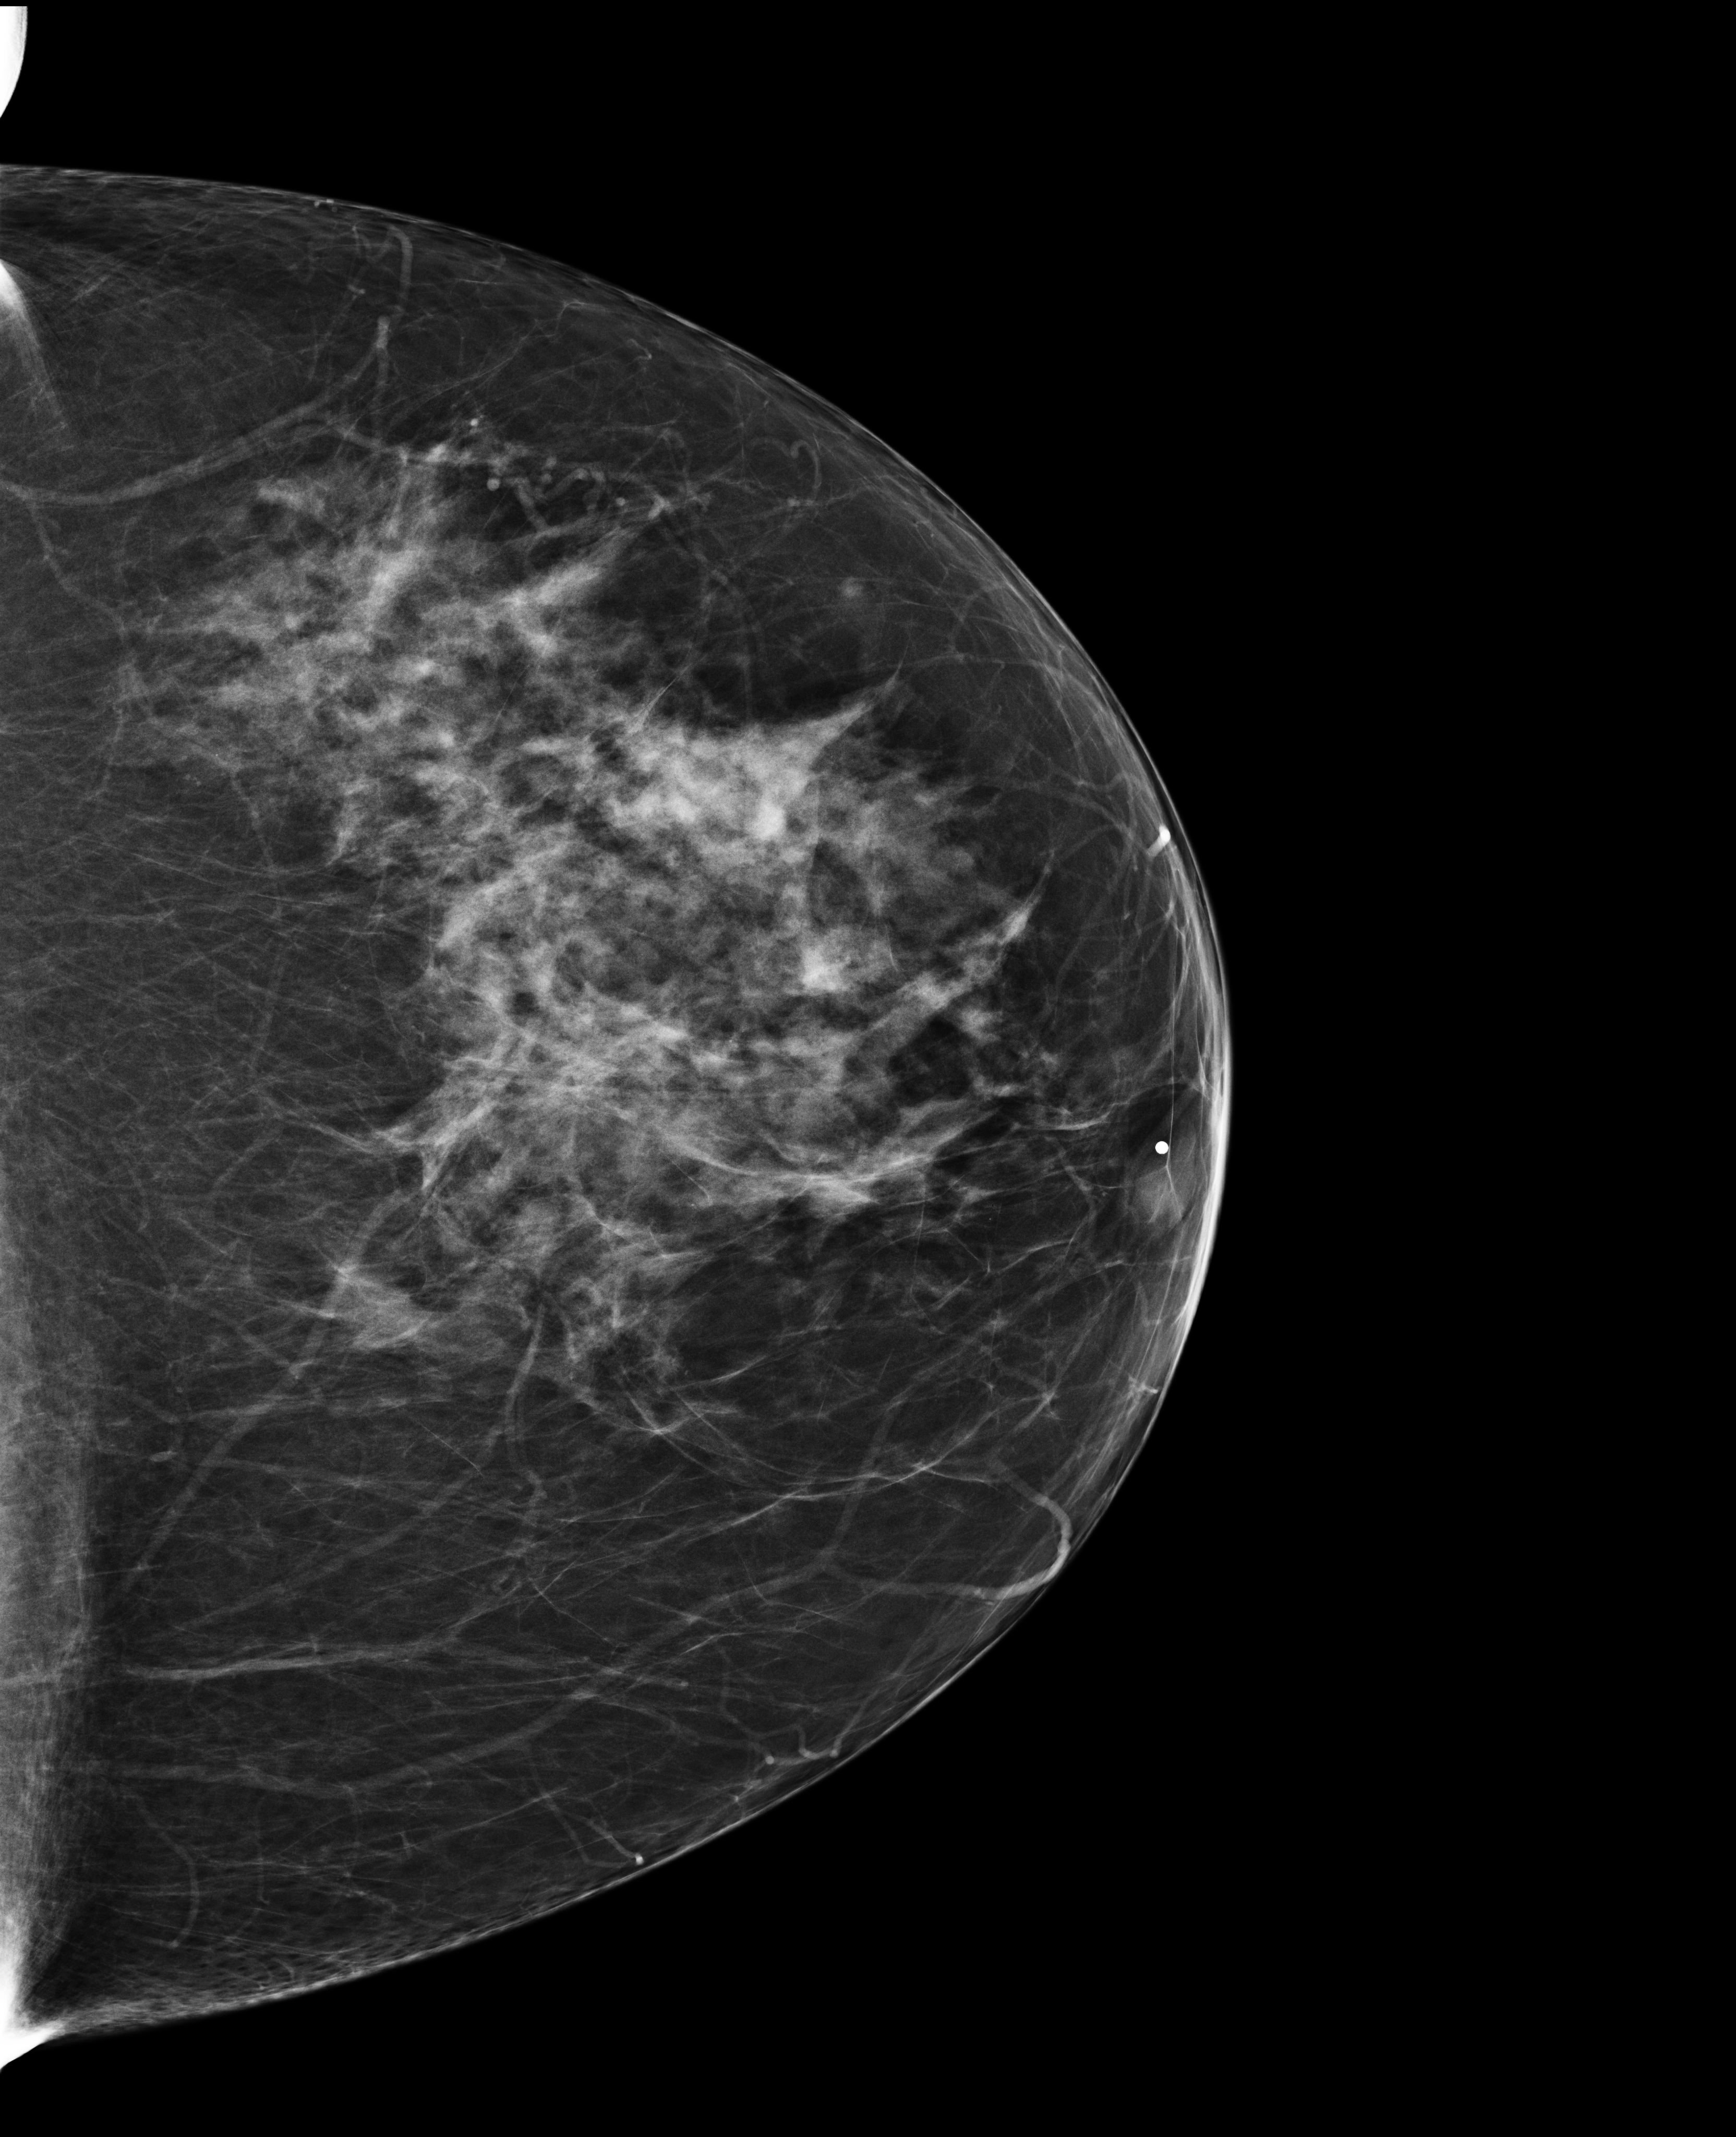
Screening examination; system: Selenia Dimensions. Patient aged 61 years (female).
Image type: full-field digital mammogram. Breast: left. Projection: cranio-caudal projection.